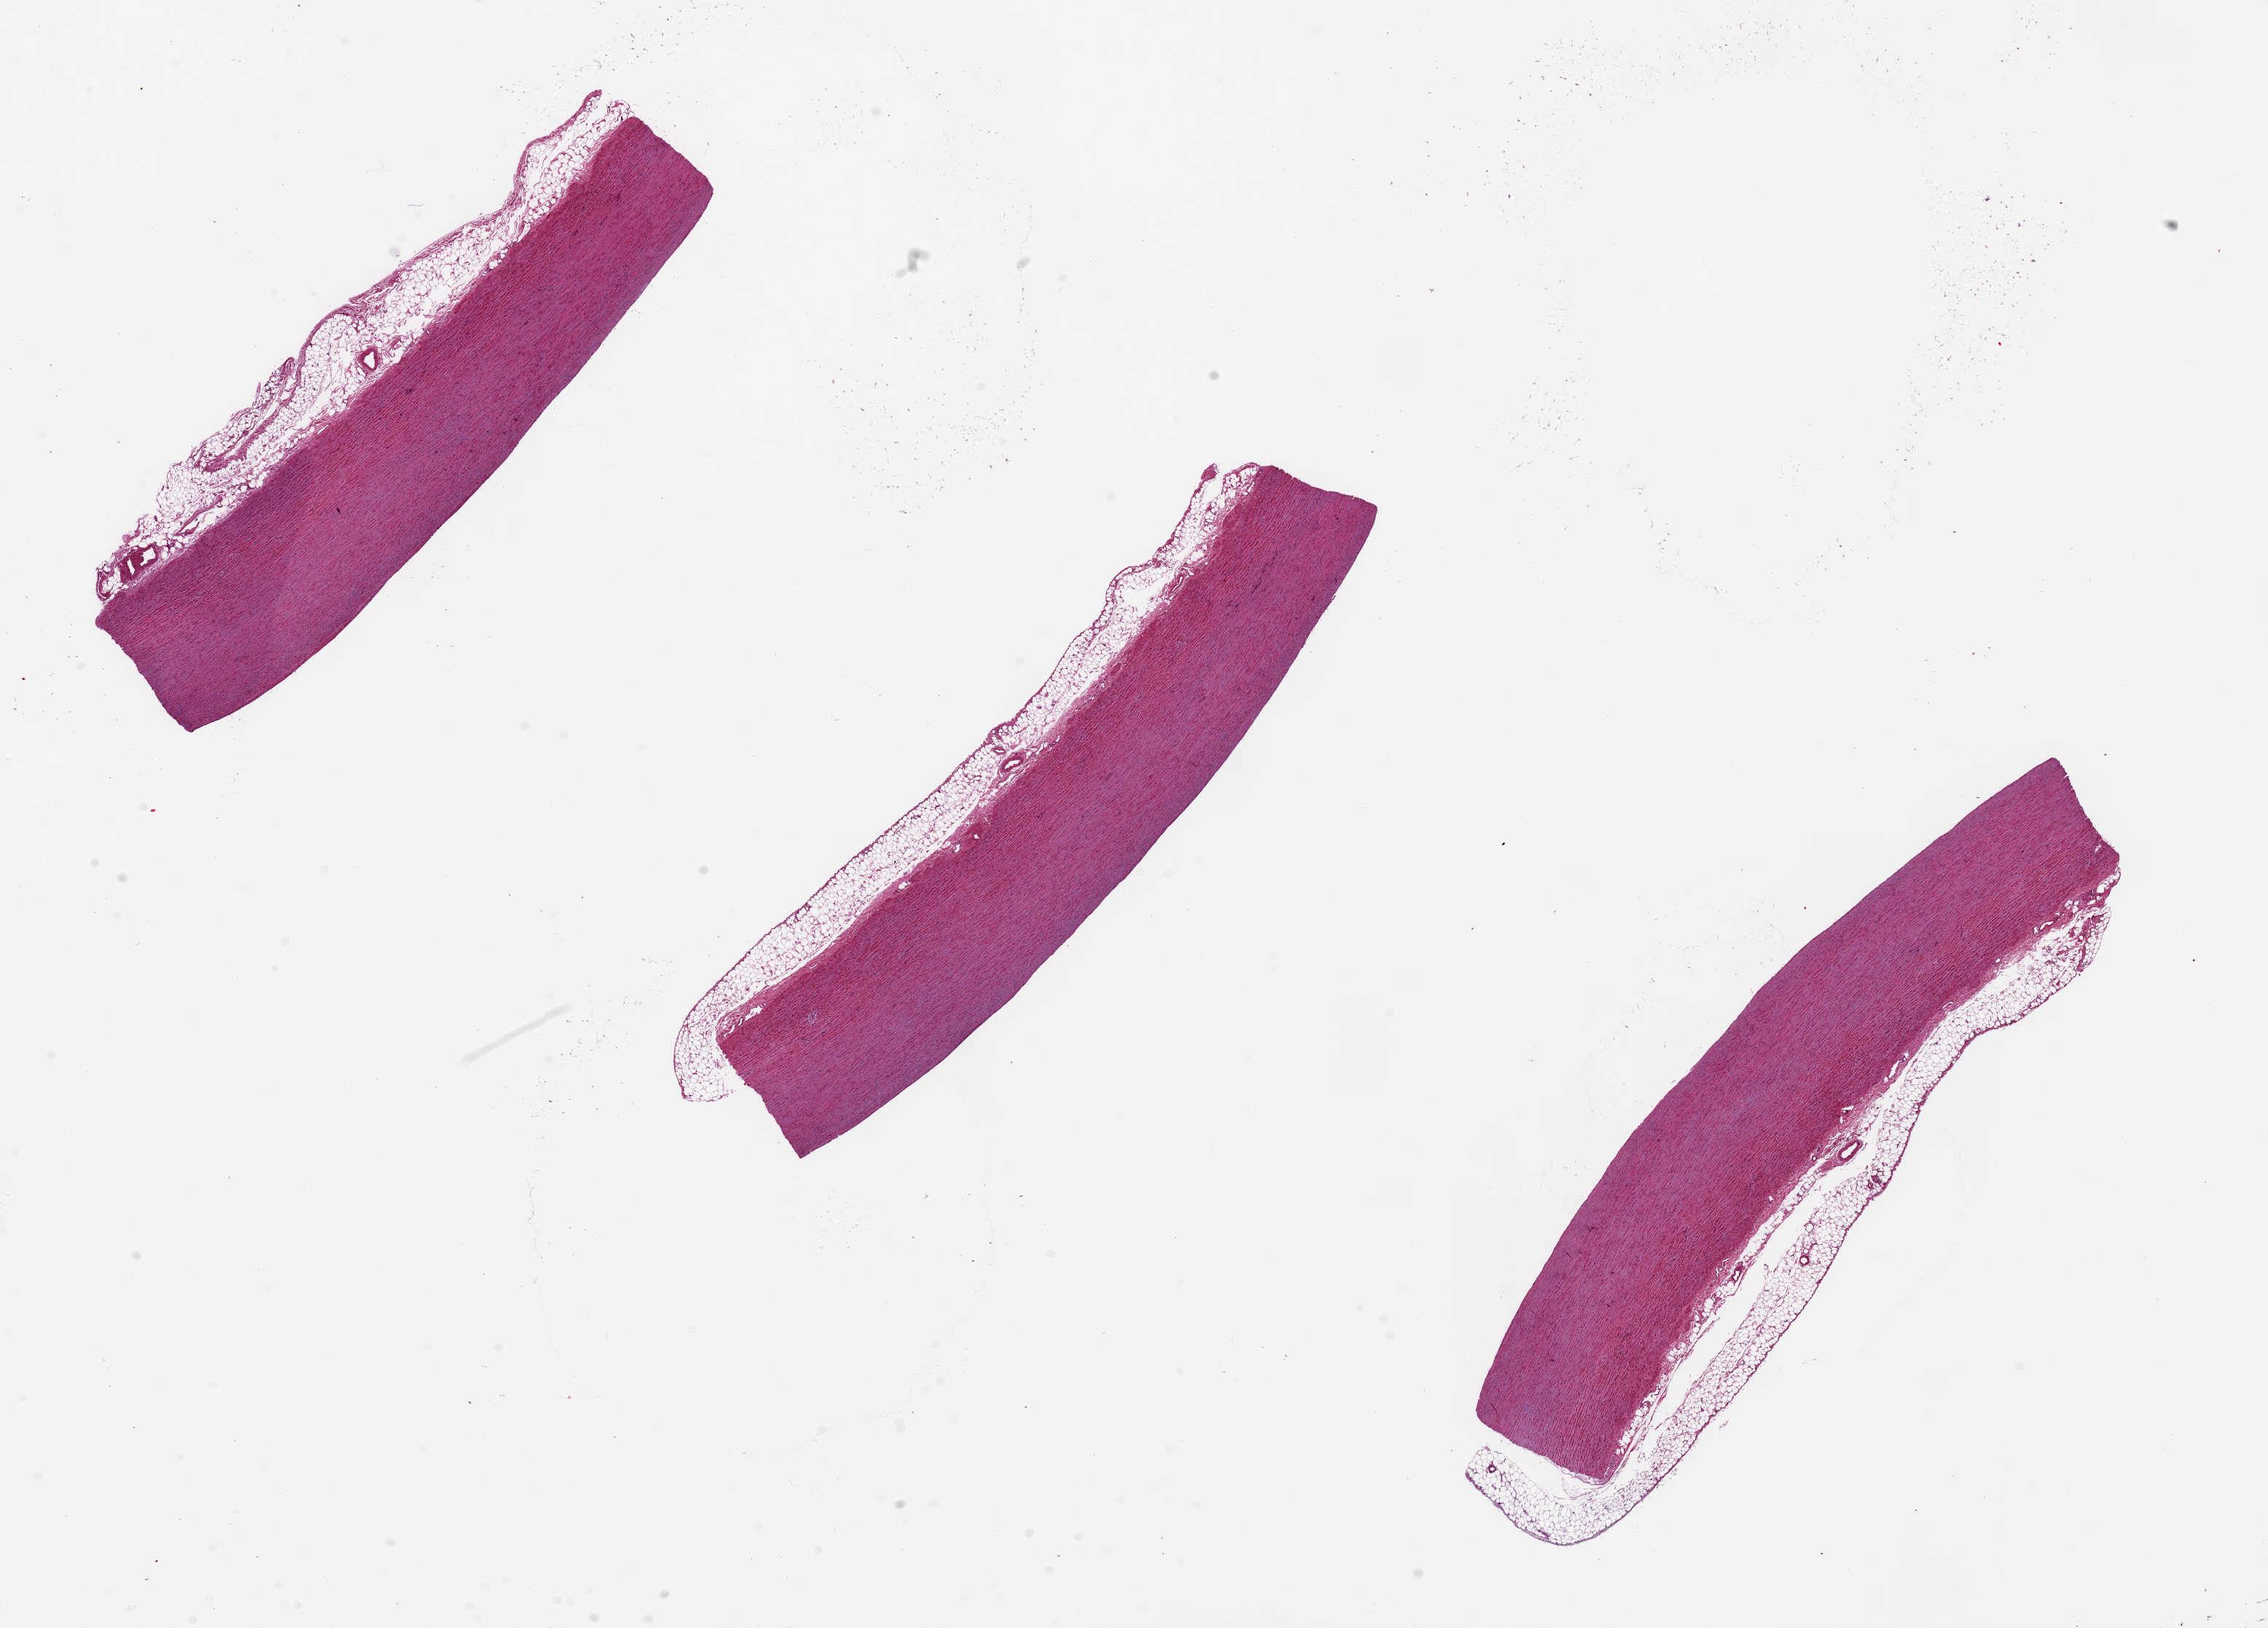
Whole-slide image, haematoxylin and eosin stain, a low-resolution overview of the entire scanned area, about 24.6 x 17.7 mm (acquisition: 20x scan). PAXgene-fixed, paraffin-embedded tissue. Target tissue: aorta. Donor tissue sample. Donor sex: male.
Reviewer comment on this tissue sample: 3 pieces, 1.7 mm thick.